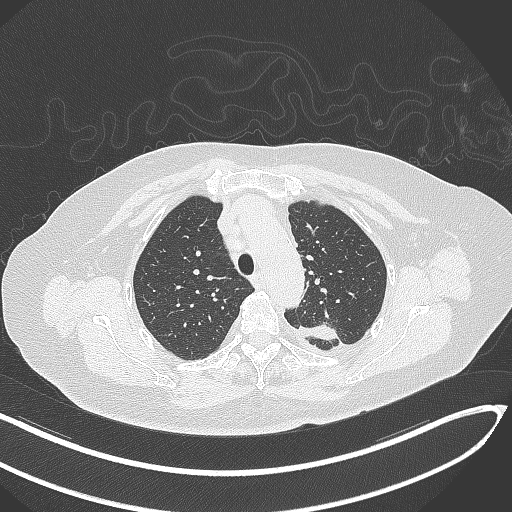
Chest CT, one axial slice; slice 243 of 270 in the series (ordered by position); reconstruction kernel B70f; 120 kVp; lung window (W 1500 / L -600 HU); 1 mm slice thickness; 512 × 512 image matrix, field of view 400 × 400 mm. Patient: female, 76 years. From the clinical record (not read from this slice): clinical TNM (as recorded): T1c N0 M0.
Annotated regions visible in this slice (rectangle marked by the reading radiologist):
- lung tumour (recorded histology: adenocarcinoma): box from (x=291, y=316) to (x=338, y=346) px